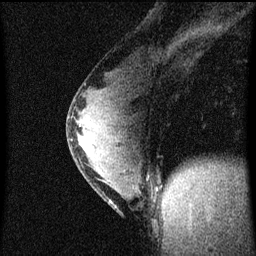
Breast MRI (dynamic contrast-enhanced), one sagittal slice; position 30 of 60 along the scan axis; dynamic contrast-enhanced series, image 2 of 4 at this slice position (ordered by acquisition); 1.5 T; TE 4.2 ms, TR 8 ms; 2 mm slice thickness; 256 × 256 image matrix. Patient: female, 33 years.
Annotated regions visible in this slice (semi-automatic segmentation, software-assisted and operator-edited):
- analysis volume of interest (the breast-tissue region the enhancement analysis was run in; not a lesion): bounding box <68,76,153,213> (left, top, right, bottom; pixels)
- tumour enhancement mask (voxels above the 70 % enhancement threshold inside the analysis volume of interest): <78,124,87,153>